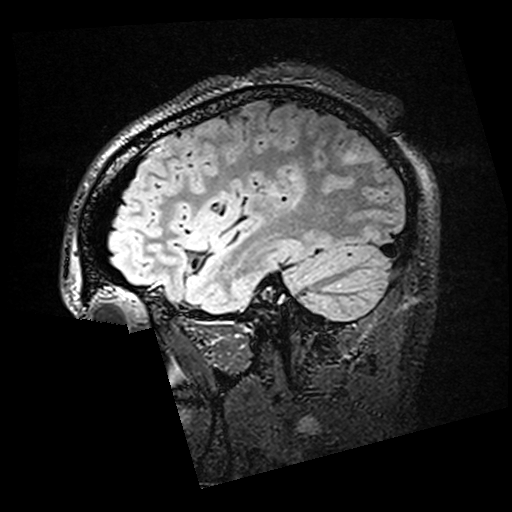
Brain MRI from a brain-tumour surgery series, one sagittal slice; position 49 of 176 along the scan axis; T2 FLAIR; 512 × 512 image matrix, field of view 250 × 250 mm. From the clinical record (not read from this slice): histopathology: Oligodendroglioma; WHO grade: 2; IDH mutation: yes; tumour location: Left Posterior Temporal.
Outlined on this slice (outlined manually by an expert reader):
- residual tumour: bounding box (x1, y1, x2, y2) in pixels: (289, 174, 293, 178)